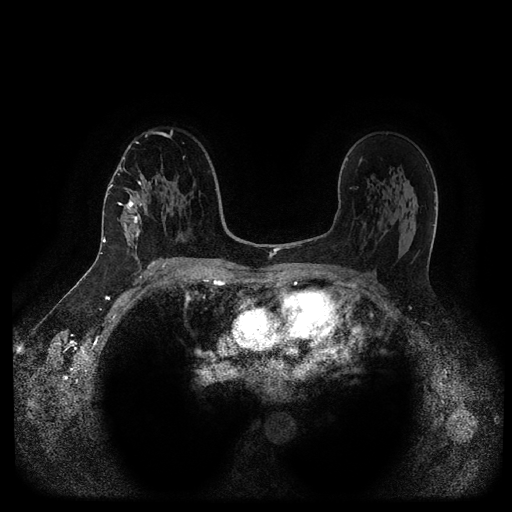
Breast MRI (dynamic contrast-enhanced, multi-phase), one axial slice; position 62 of 116 along the scan axis; dynamic contrast-enhanced series, time point 2 of 5 at this slice position (early post-contrast); 1.5 T; TE 2.6 ms, TR 5.3 ms; 2 mm slice thickness; 512 × 512 image matrix, field of view 360 × 360 mm. Female patient, age 58 years.
Outlined on this slice (semi-automatically segmented with operator editing):
- breast lesion (labelled 'tumour' in the annotation; benign lesions carry a separate 'benign' label): bounding box <115,187,148,253> (left, top, right, bottom; pixels)